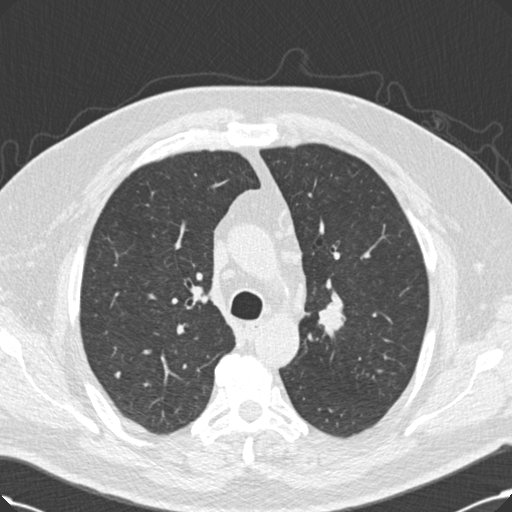
Low-dose screening chest CT, one axial slice. Position 155 of 214 along the scan axis. Reconstruction kernel B30f. Lung window (W 1500 / L -600 HU). 2 mm slice thickness. 512 × 512 image matrix, field of view 365 × 365 mm.
Annotated regions visible in this slice (expert manual segmentation):
- lesion 1 (tumor): bounding box (x1, y1, x2, y2) in pixels: (319, 292, 345, 337)